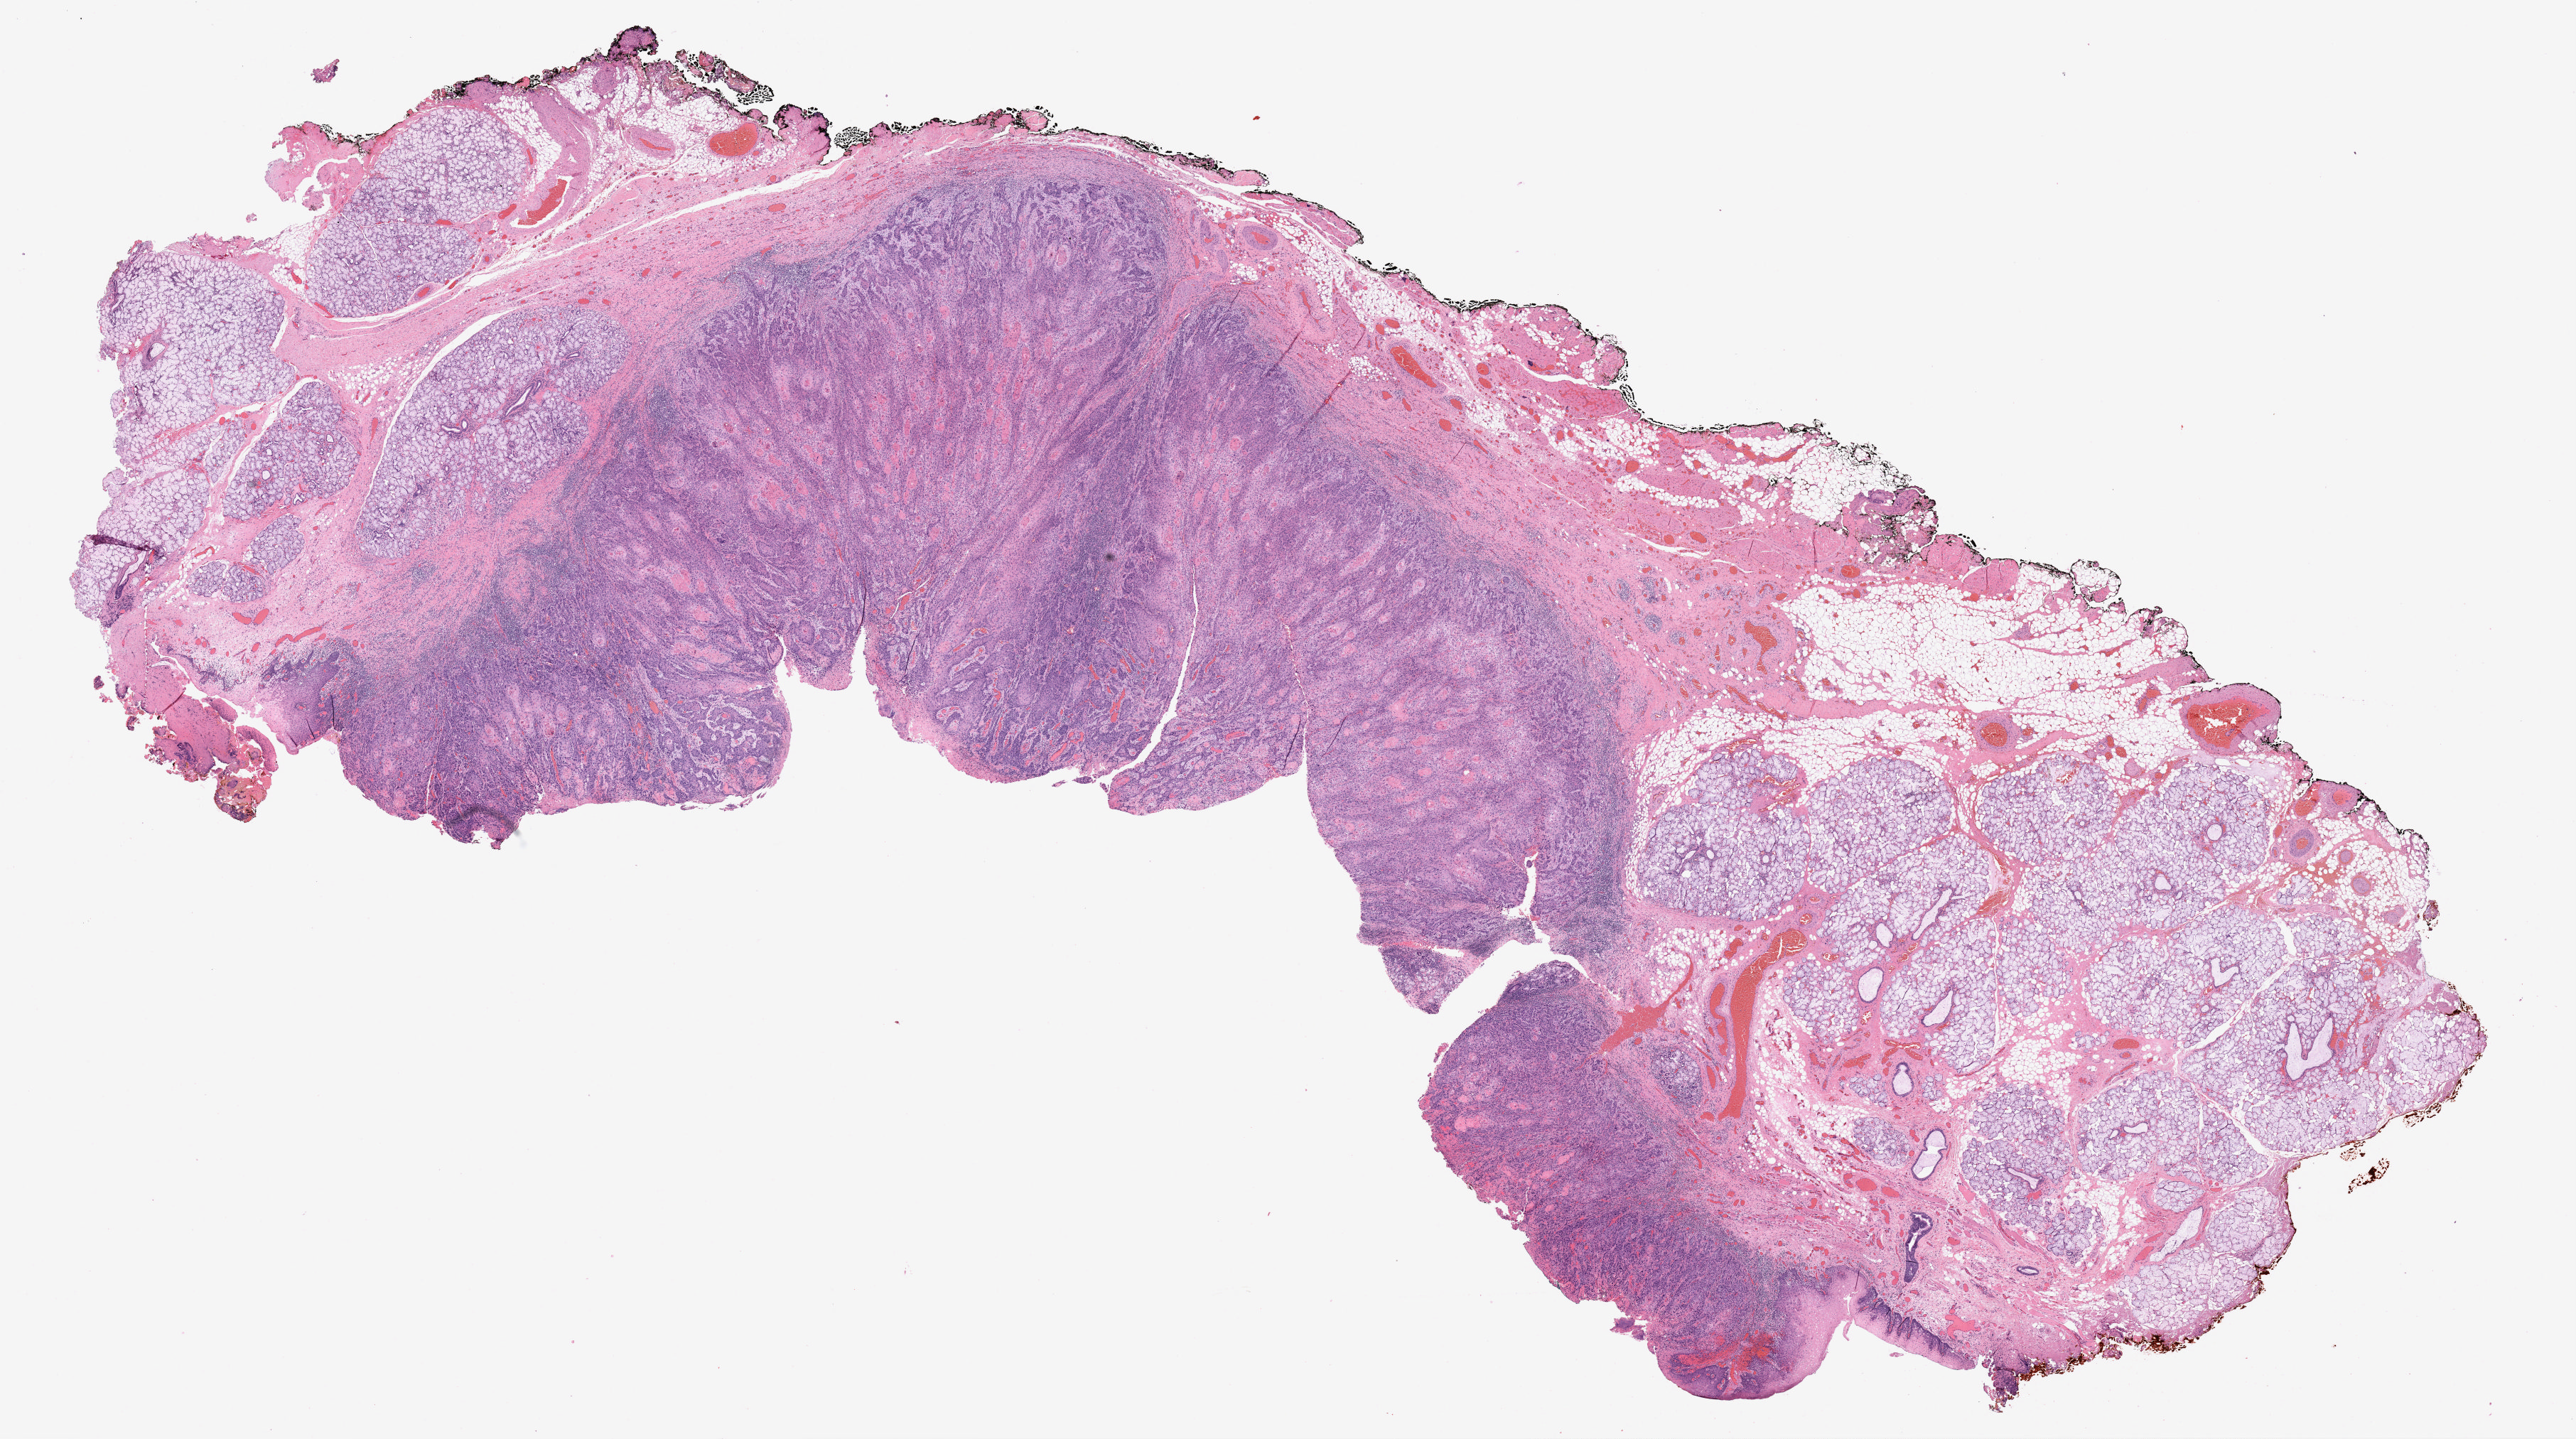
H&E whole-slide image — a low-resolution overview of the entire scanned area, about 28.9 x 16.2 mm (slide scanned at 20x); formalin-fixed paraffin-embedded (FFPE) diagnostic section; head and neck, primary tumour sample. Female, age 52 years at initial diagnosis. Histologic grade: G2 (moderately differentiated).
Histologic diagnosis: Squamous cell carcinoma, NOS. AJCC pathologic stage: I.